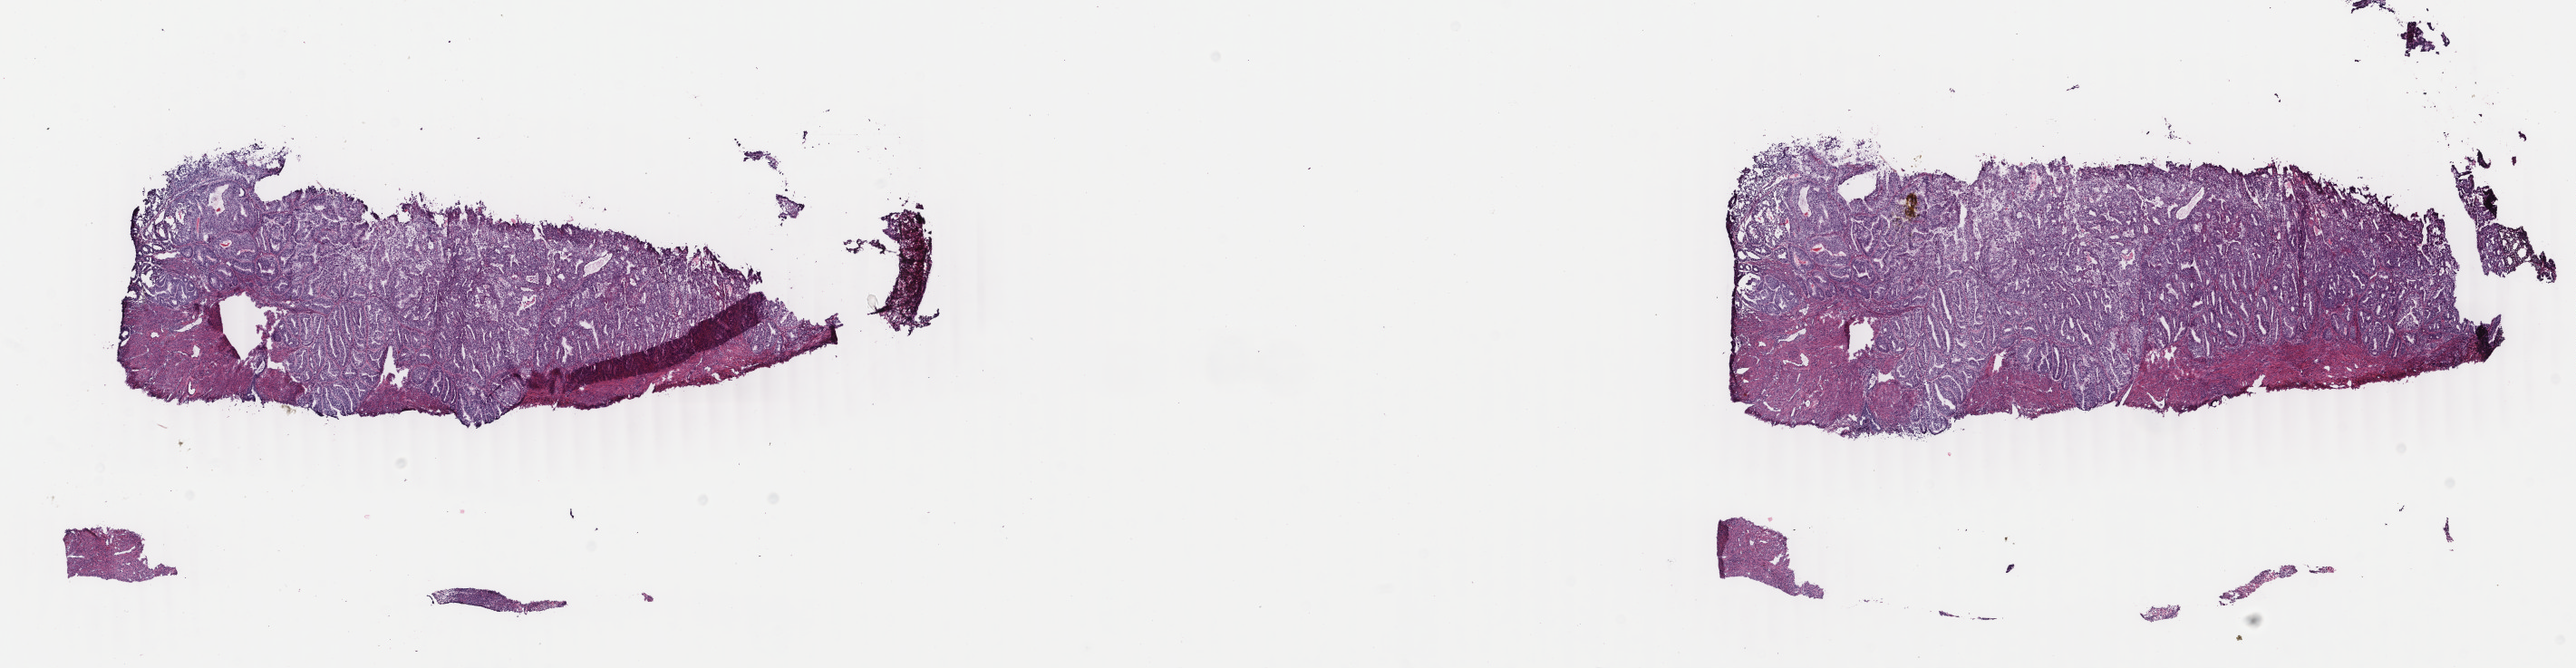
H&E whole-slide image — low-resolution overview of the scanned area, about 22.6 x 5.9 mm; frozen section from the bottom of the tissue portion; sample: primary tumour, uterus. Female, age 87 years at initial diagnosis. Histologic grade: G1 (well differentiated). Composition of this section per pathologist review: tumour cells 85%, tumour nuclei 70%, normal cells 0%, stromal cells 15%, necrosis 0%. Infiltration values recorded for this section: lymphocyte infiltration 0%, monocyte infiltration 0%, neutrophil infiltration 0%.
FIGO stage: IB. Pathologic diagnosis: Endometrioid adenocarcinoma, NOS (endometrium).